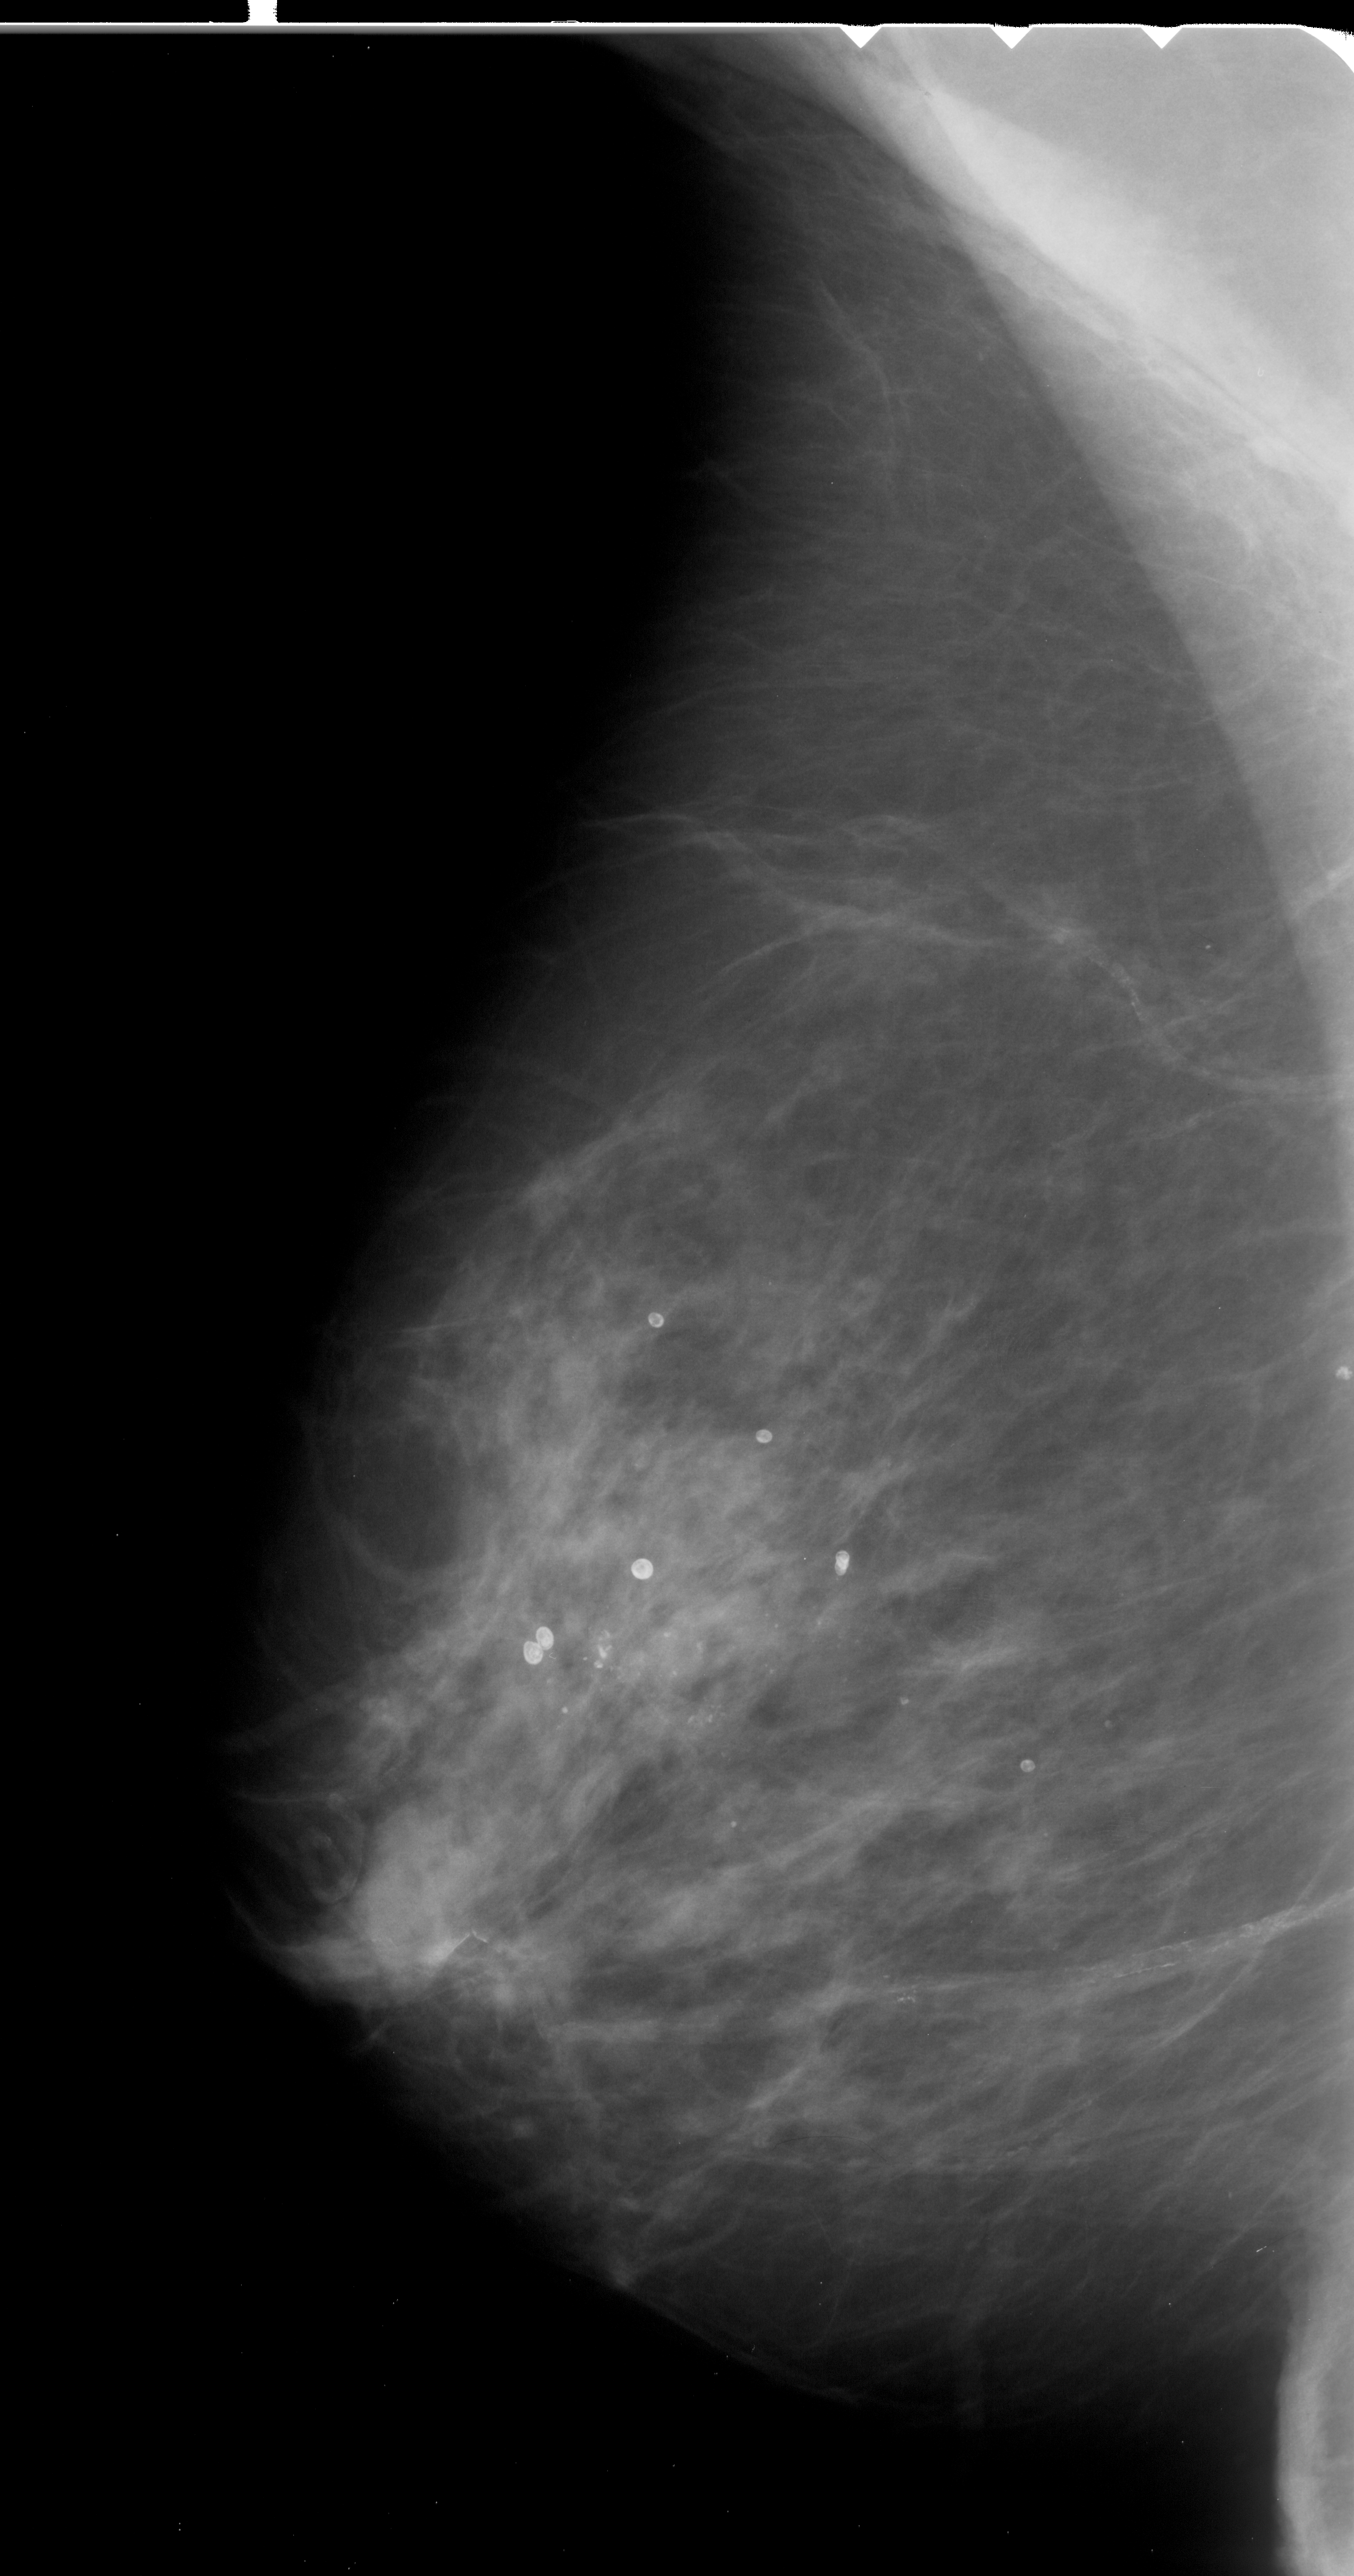
Mammogram (digitized film), left breast, MLO view, BI-RADS breast density category 3 (scale 1–4).
Radiologist-marked abnormalities on this image: calcifications, morphology pleomorphic, distribution segmental; BI-RADS assessment category 4; pathology (as recorded): malignant.